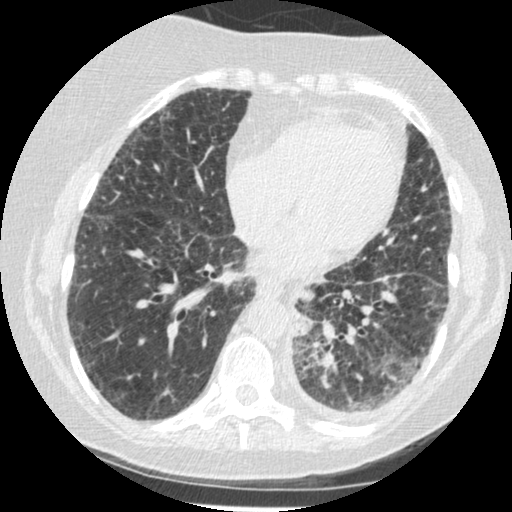
Low-dose screening chest CT, one axial slice. Slice 72 of 341 in the series (ordered by position). Reconstruction kernel STANDARD. 120 kVp. Lung window (W 1500 / L -600 HU). 1.25 mm slice thickness. 512 × 512 image matrix, field of view 310 × 310 mm.
Annotated regions visible in this slice (manually delineated by an expert):
- lesion 1 (tumor, lower lobe of left lung): bounding box (x1, y1, x2, y2) in pixels: (294, 324, 308, 335)